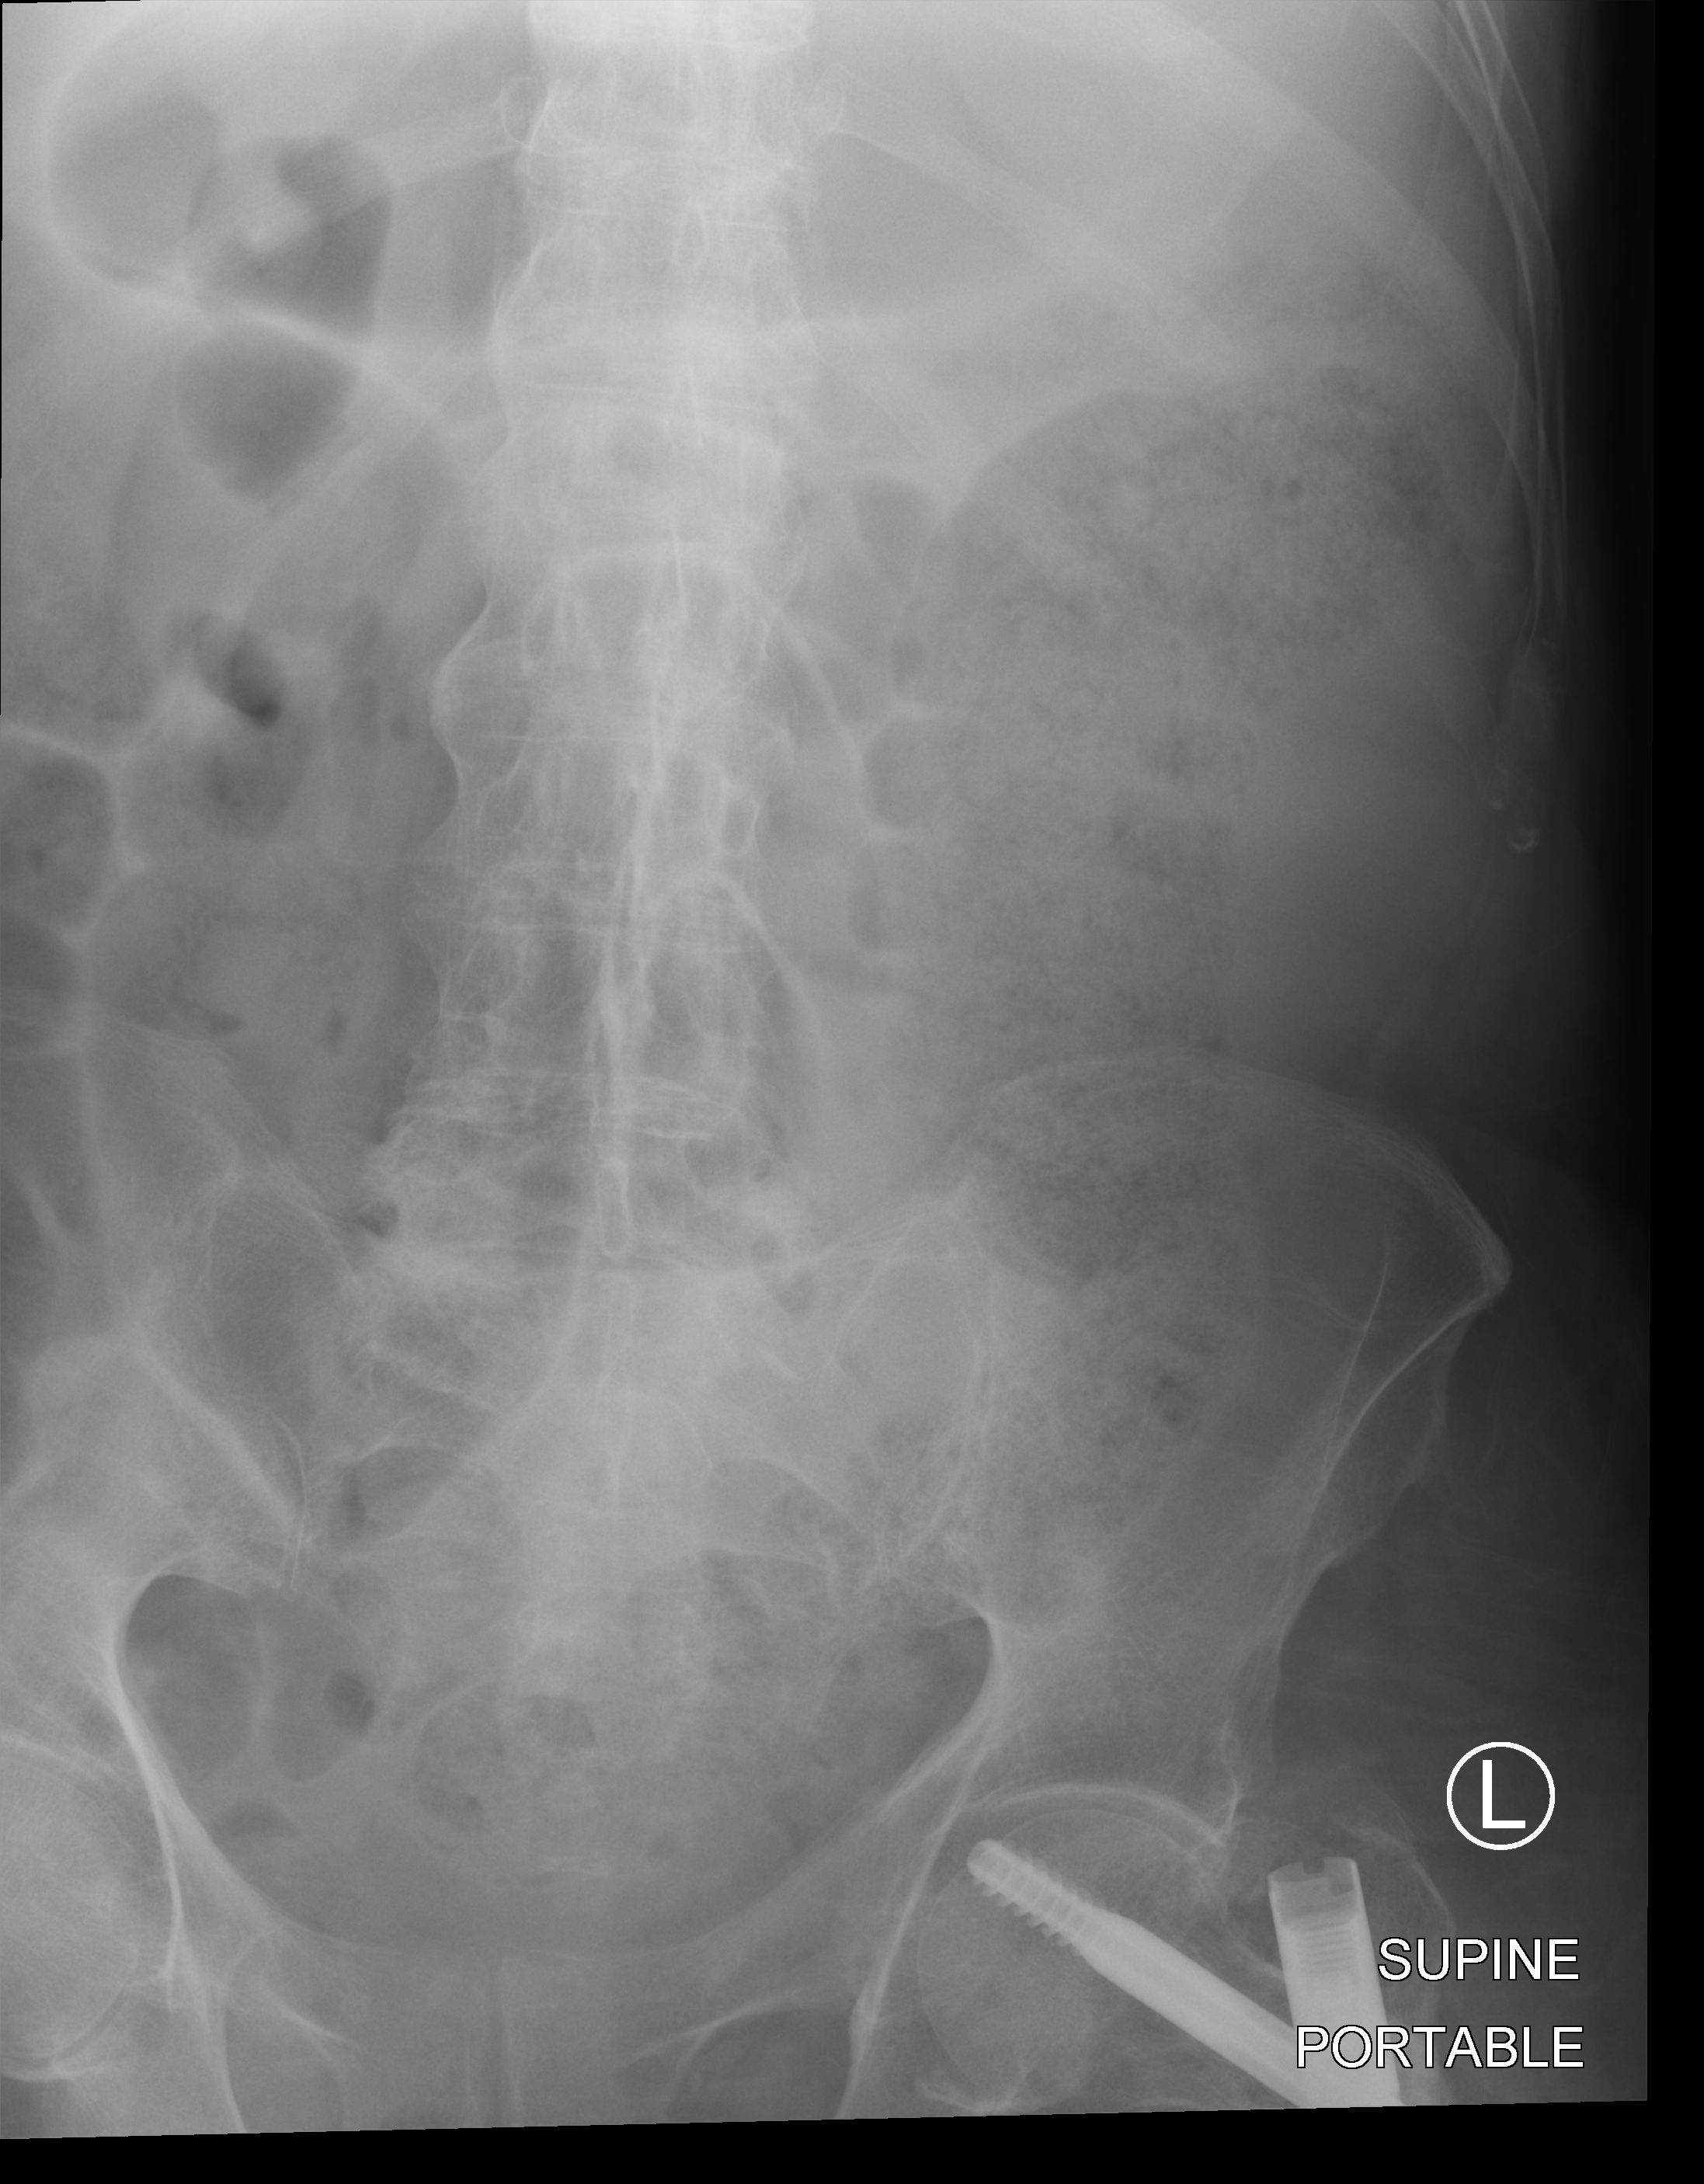
Abdomen X-ray (portable); anteroposterior (AP) projection. Male patient hospitalised with COVID-19, age 75–90 years.
From the hospital-stay record, not from the radiograph (when in the stay this image was taken is not recorded):
- admitted to intensive care during this hospital stay: no
- mechanically ventilated during this hospital stay: no